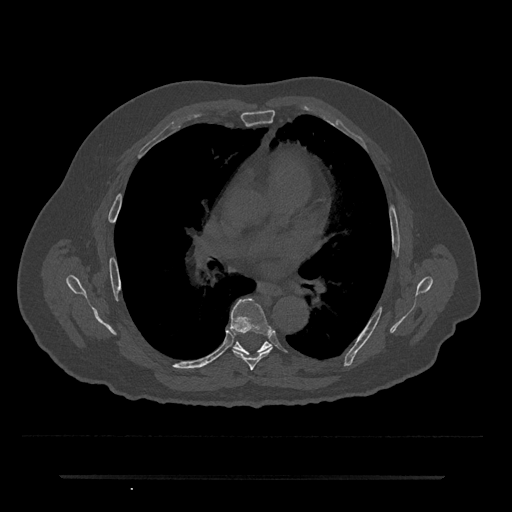
CT including the spine, one axial slice; position 418 of 797 along the scan axis; reconstruction kernel Br40s/3; bone window (W 1800 / L 400 HU); 512 × 512 image matrix, field of view 437 × 437 mm. Male patient, age 69 years. From the clinical record (not read from this slice): primary cancer: prostate.
Structures marked on this image (semi-automatic segmentation, software-assisted and operator-edited):
- T6 vertebra: box from (x=230, y=299) to (x=274, y=371) px
- T7 vertebra: (x=233, y=342)–(x=271, y=355)